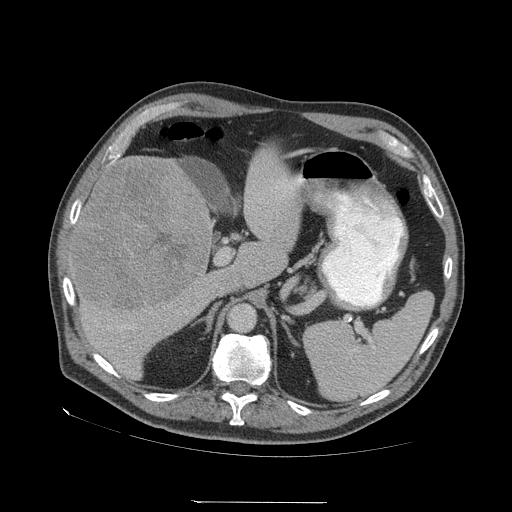
Contrast-enhanced abdominal CT (liver protocol), one axial slice. Slice 34 of 83 in the series (ordered by position). Soft-tissue window (W 400 / L 40 HU). 512 × 512 image matrix, field of view 460 × 460 mm. Case-level facts recorded for this patient, not image findings: diagnosis: hepatocellular carcinoma (patient treated with transarterial chemoembolisation; whether this scan precedes or follows treatment is not stated here); TNM stage (as recorded): Stage-I; Child-Pugh class: A.
Outlined on this slice (semi-automatically segmented with operator editing):
- liver parenchyma outside the tumour (the mass and vessels are separate outlines, so this box may not span the whole liver): bounding box [x1, y1, x2, y2] px = [68, 156, 282, 380]
- mass: [72, 156, 211, 310]